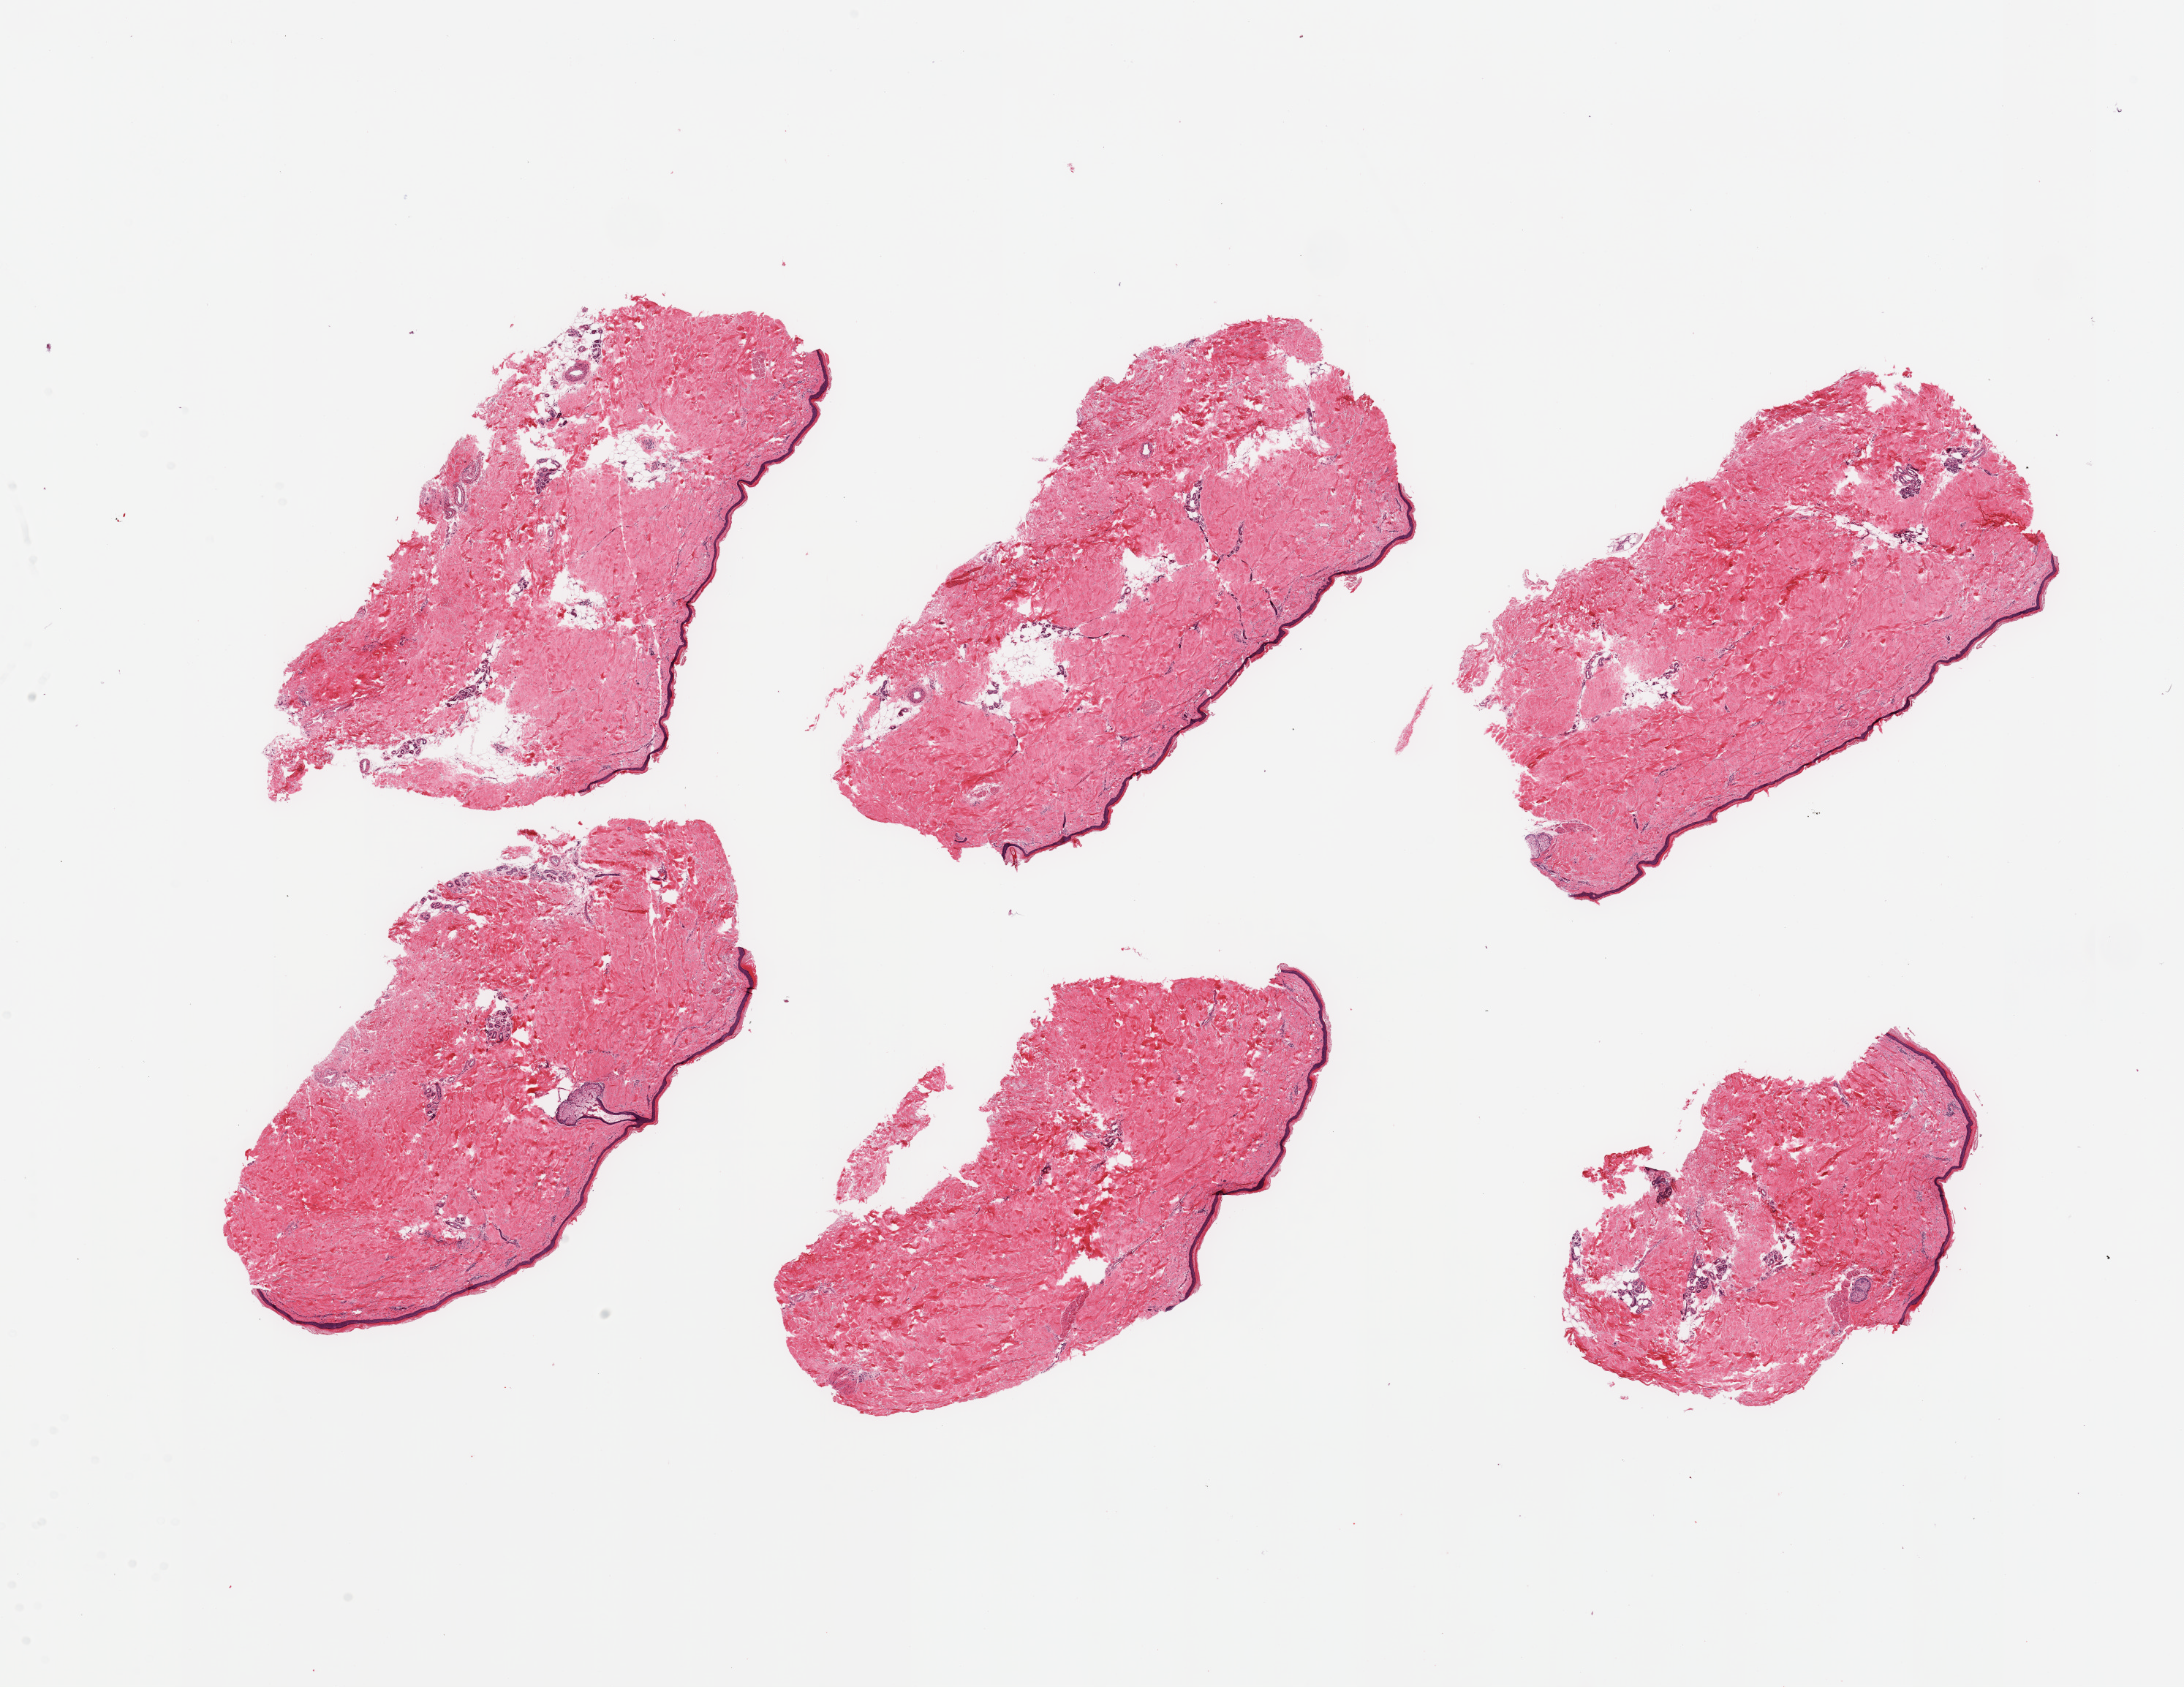
Whole-slide image, haematoxylin and eosin stain, a low-resolution overview of the entire scanned area, about 23.6 x 18.2 mm (from a 20x scan); PAXgene-fixed, paraffin-embedded tissue; target tissue: skin of lower leg; tissue donor sample. Male donor.
Pathologist's review note for this sample: 6 pieces, no significant dermal fat, squamous epithelium is ~30-40 microns.